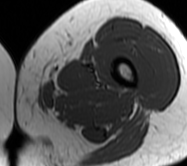
MRI of an extremity soft-tissue mass, one axial slice; slice 4 of 62 in the series (ordered by position); MR volume resampled by the dataset authors to the PET/CT grid (not the native acquisition matrix); 3.27 mm slice thickness; 187 × 166 image matrix, field of view 183 × 162 mm. Female patient. Case-level facts recorded for this patient, not image findings: histological type: leiomyosarcoma; grade: high; site of the primary tumour: groin.
Annotated regions visible in this slice (expert contour drawn on MRI and transferred to this co-registered scan by the dataset authors):
- gross tumour volume including surrounding oedema: bounding box (x1, y1, x2, y2) in pixels: (16, 96, 44, 113)